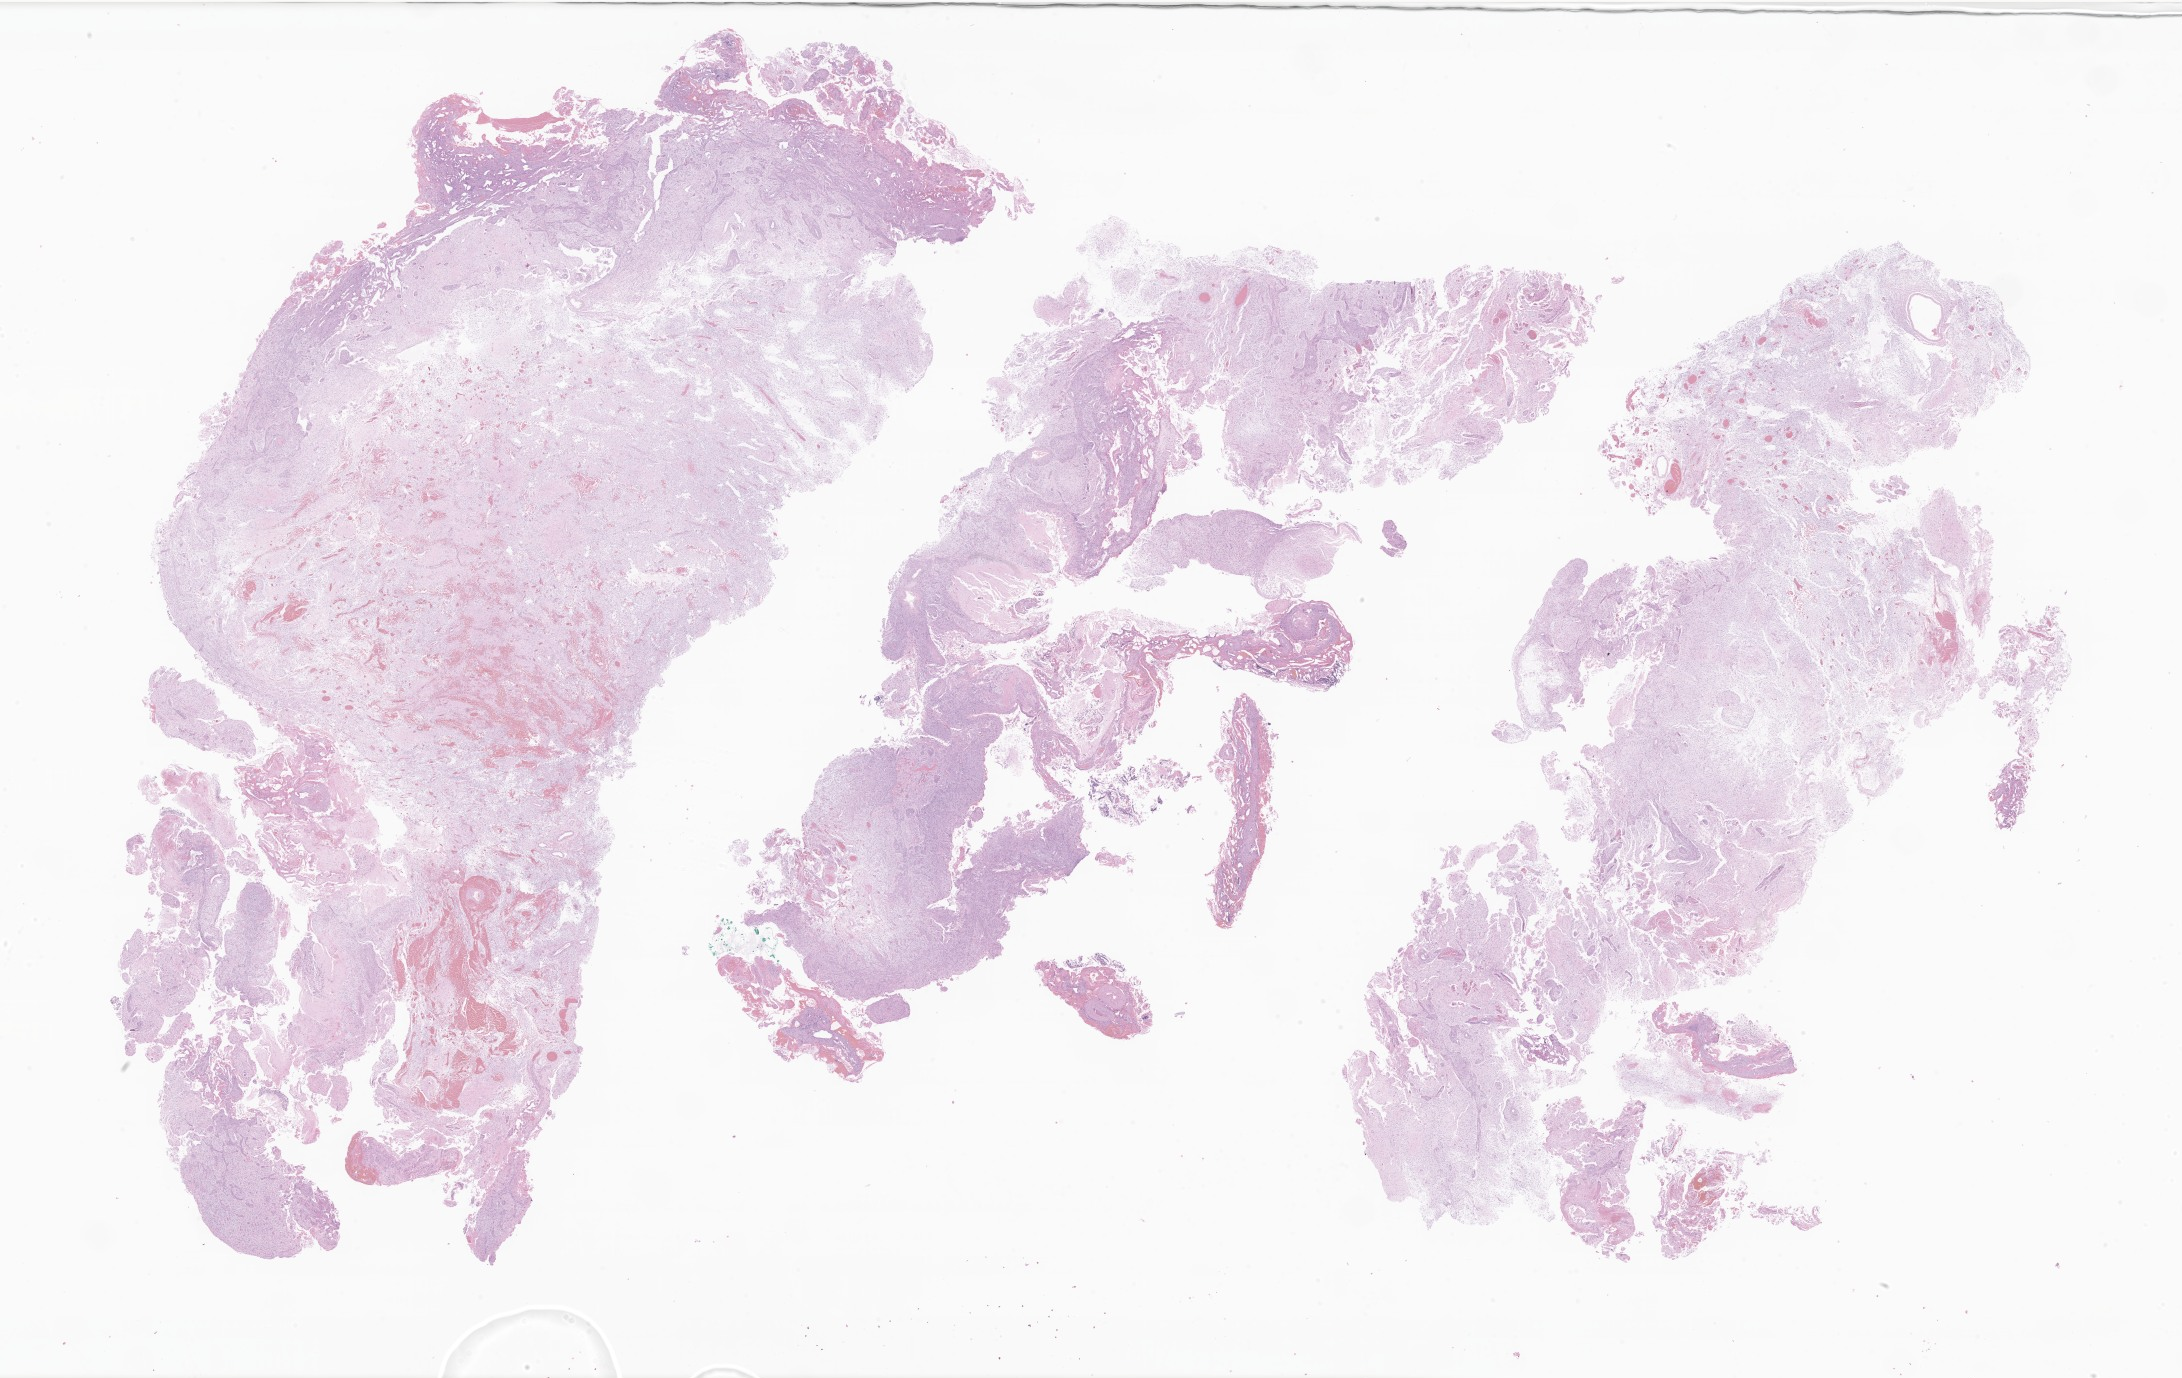
Whole-slide image, hematoxylin and eosin (H&E) stain of tumor tissue from the brain — shown as a low-resolution overview of the whole scanned area (about 36.8 x 23.2 mm); formalin-fixed paraffin-embedded section. Patient female; age 65 months (5 years 5 months).
Diagnosis: Neoplasm, malignant.